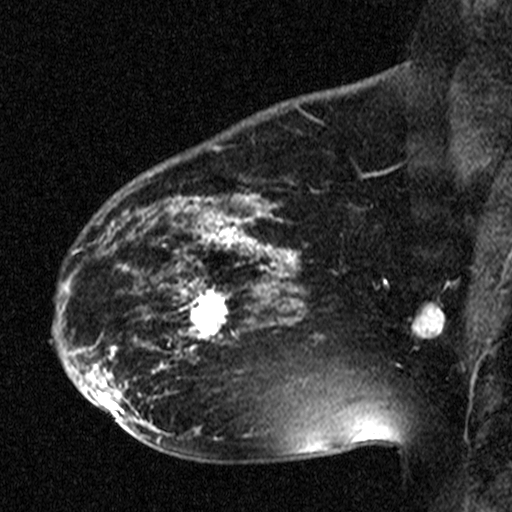
Breast MRI (dynamic contrast-enhanced), one sagittal slice. Position 30 of 44 along the scan axis. Dynamic contrast-enhanced study with each time point stored as its own series, time point 2 of 3 at this slice position (early post-contrast, ordered by acquisition time). 1.5 T. TE 4.5 ms, TR 11 ms. 3 mm slice thickness. 512 × 512 image matrix. Patient: female, 38 years. From the clinical record (not read from this slice): setting: breast cancer imaged before/during neoadjuvant chemotherapy; receptor status: HR-positive, HER2-negative.
Outlined on this slice (semi-automatic segmentation, software-assisted and operator-edited):
- analysis volume of interest (the breast-tissue region the enhancement analysis was run in; not a lesion): bounding box (x1, y1, x2, y2) in pixels: (176, 272, 251, 349)
- tumour enhancement mask (voxels above the 90 % enhancement threshold inside the analysis volume of interest): (176, 273, 251, 347)